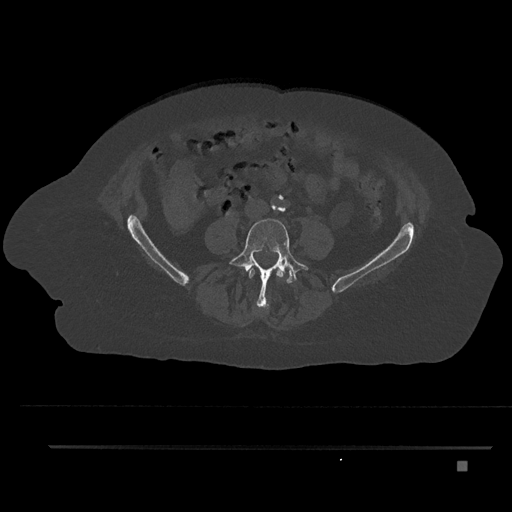
CT including the spine, one axial slice; slice 83 of 797 in the series (ordered by position); reconstruction kernel Br40s/3; 120 kVp; bone window (W 1800 / L 400 HU); 512 × 512 image matrix, field of view 437 × 437 mm. Patient: female, 76 years. Case-level facts recorded for this patient, not image findings: primary cancer: lung; vertebrae with lytic lesions (as recorded): T11, L3.
Structures marked on this image (semi-automatically segmented with operator editing):
- L3 vertebra: box from (x=249, y=268) to (x=284, y=279) px
- L4 vertebra: (x=229, y=218)–(x=309, y=312)
- L5 vertebra: (x=287, y=268)–(x=294, y=283)